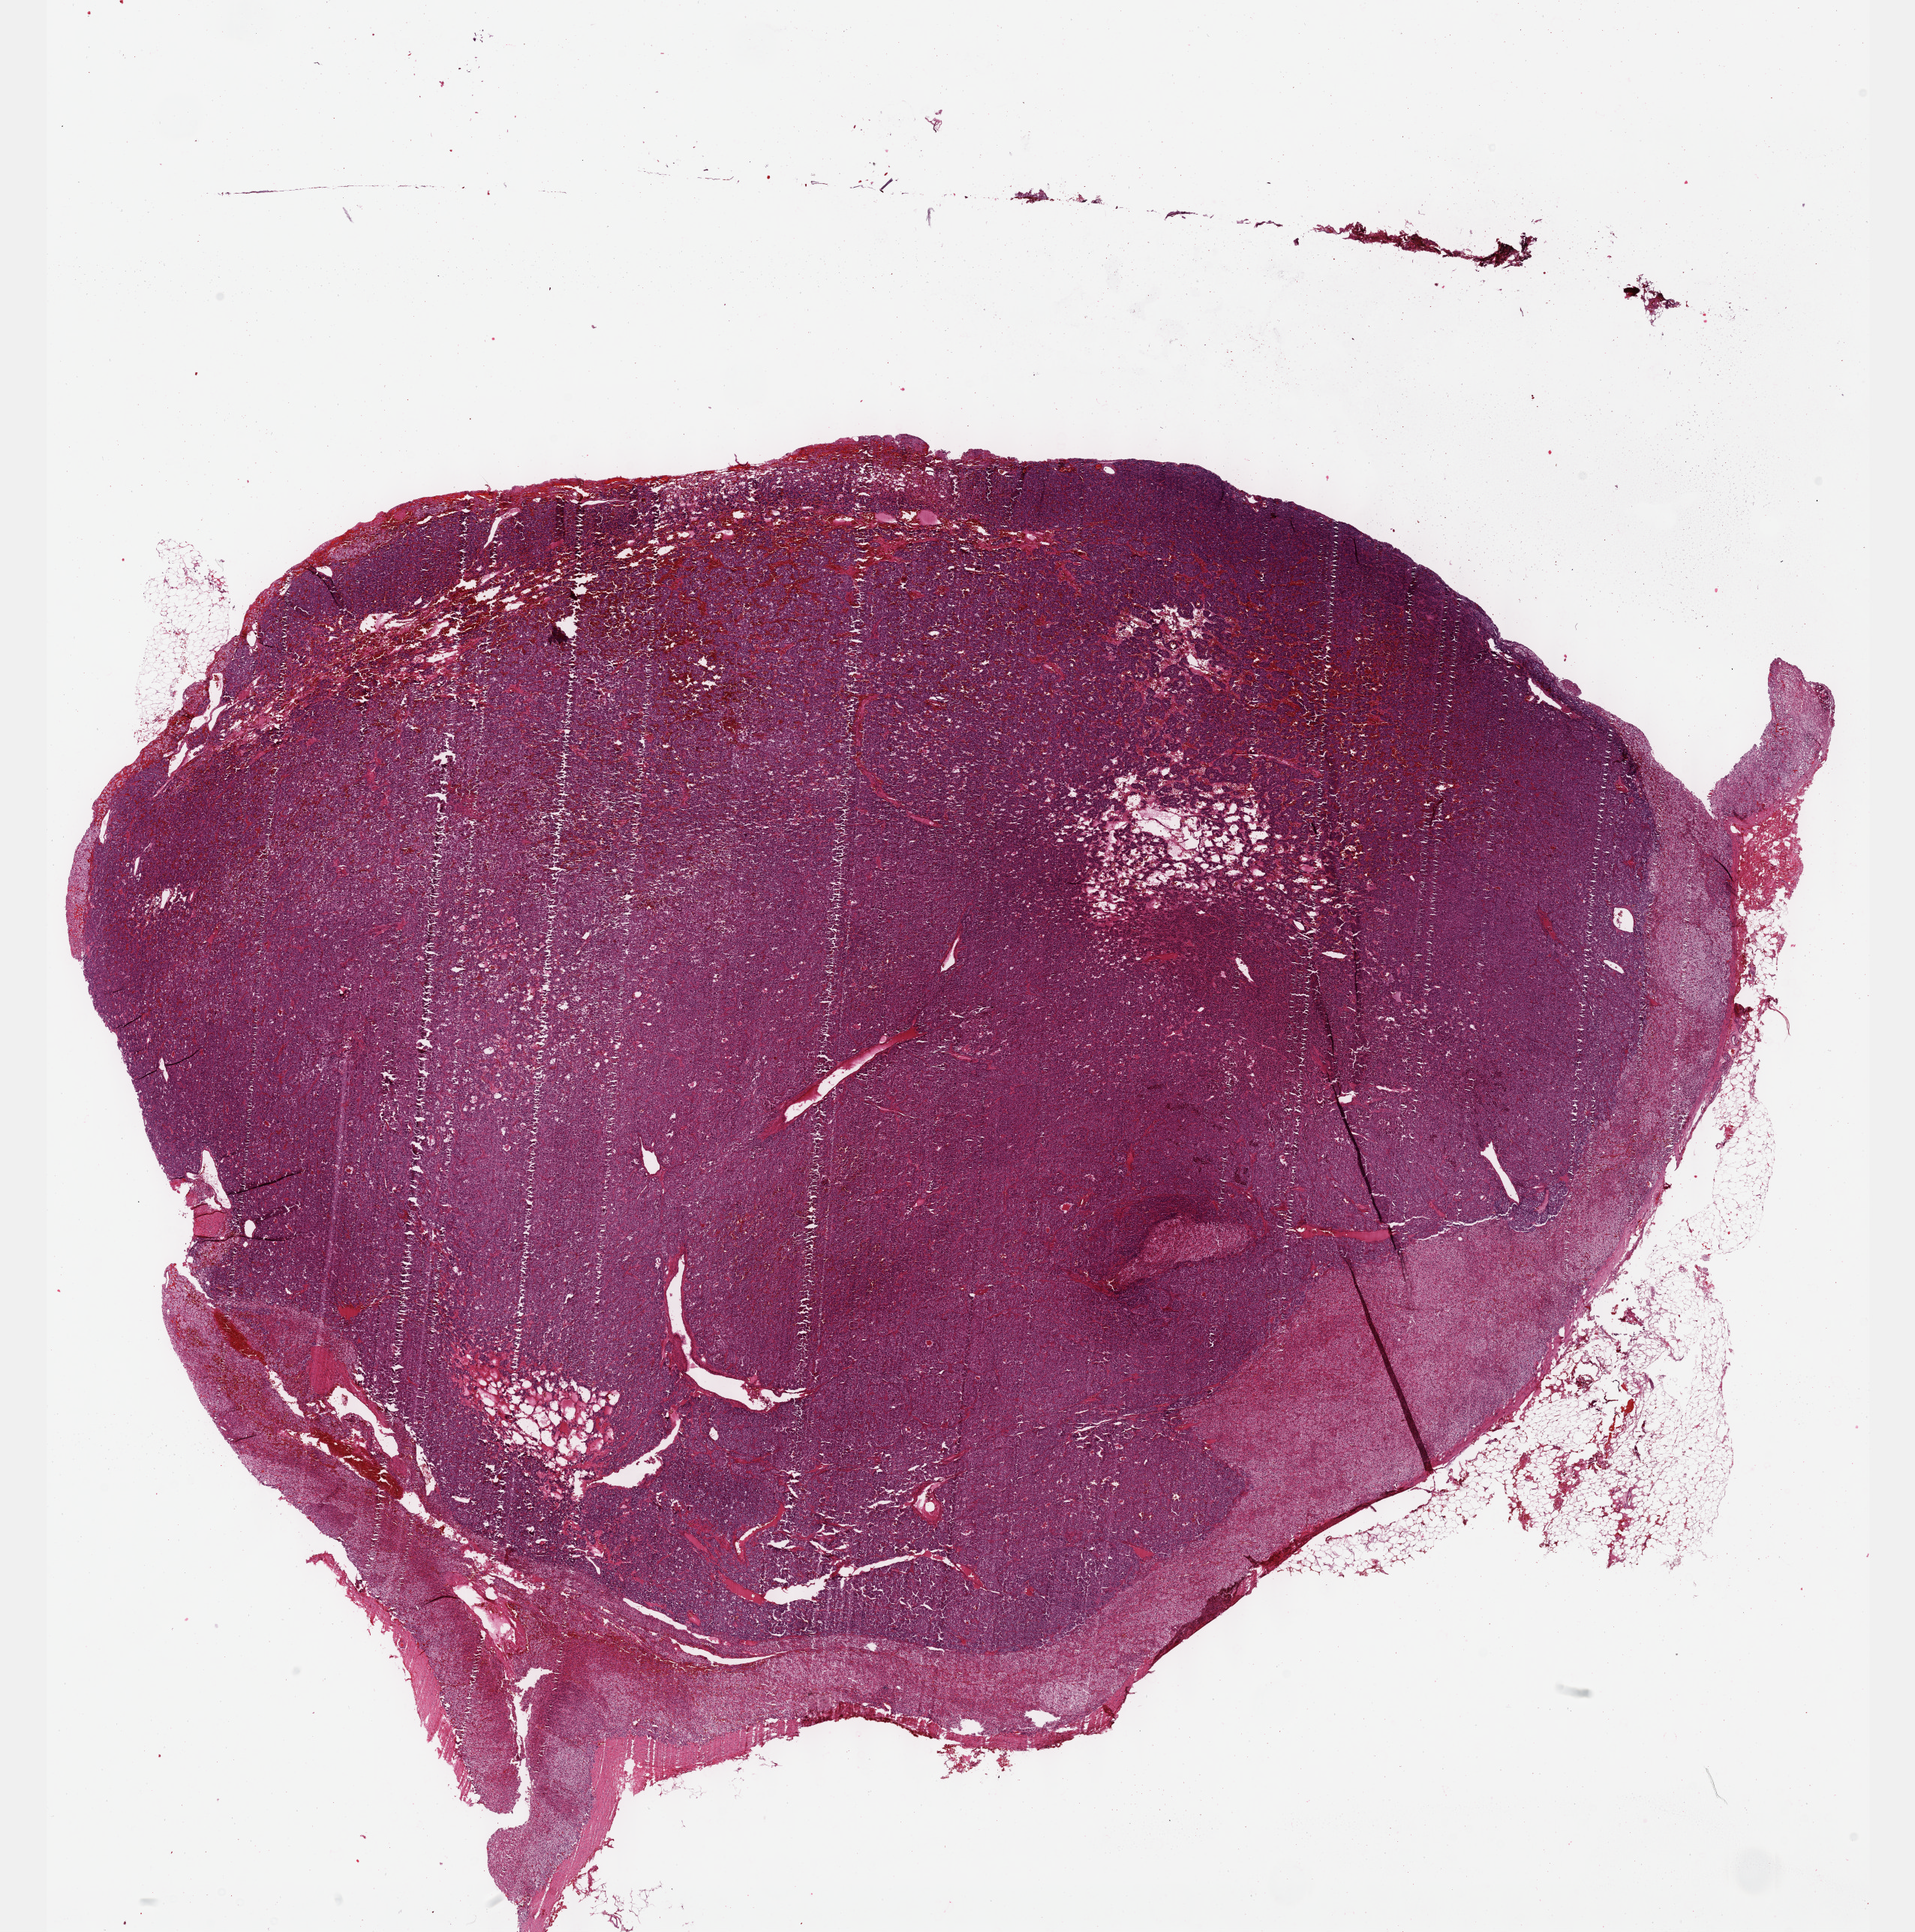
Digitized Hematoxylin and eosin (H&E) stained tissue section (whole slide) — shown as a low-resolution overview of the whole scanned area (about 20.6 x 20.8 mm, slide scanned at 40x); formalin-fixed paraffin-embedded (FFPE) diagnostic section; adrenal gland, primary tumour sample. Male, age 64 years at initial diagnosis.
Pathologic diagnosis: Pheochromocytoma, NOS.